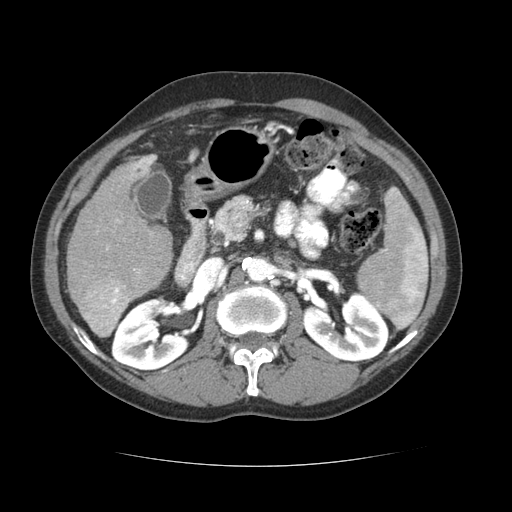
Contrast-enhanced abdominal CT (liver protocol), one axial slice; position 31 of 69 along the scan axis; reconstruction kernel STANDARD; soft-tissue window (W 400 / L 40 HU); 2.5 mm slice thickness; 512 × 512 image matrix, field of view 360 × 360 mm. From the clinical record (not read from this slice): diagnosis: hepatocellular carcinoma (patient treated with transarterial chemoembolisation; whether this scan precedes or follows treatment is not stated here); TNM stage (as recorded): Stage-II; Child-Pugh class: B; tumour differentiation: poorly differentiated.
Structures marked on this image (semi-automatically segmented with operator editing):
- liver parenchyma outside the tumour (the mass and vessels are separate outlines, so this box may not span the whole liver): box from (x=66, y=154) to (x=172, y=336) px
- mass: (x=79, y=273)–(x=132, y=334)
- liver vessels: (x=106, y=155)–(x=155, y=272)